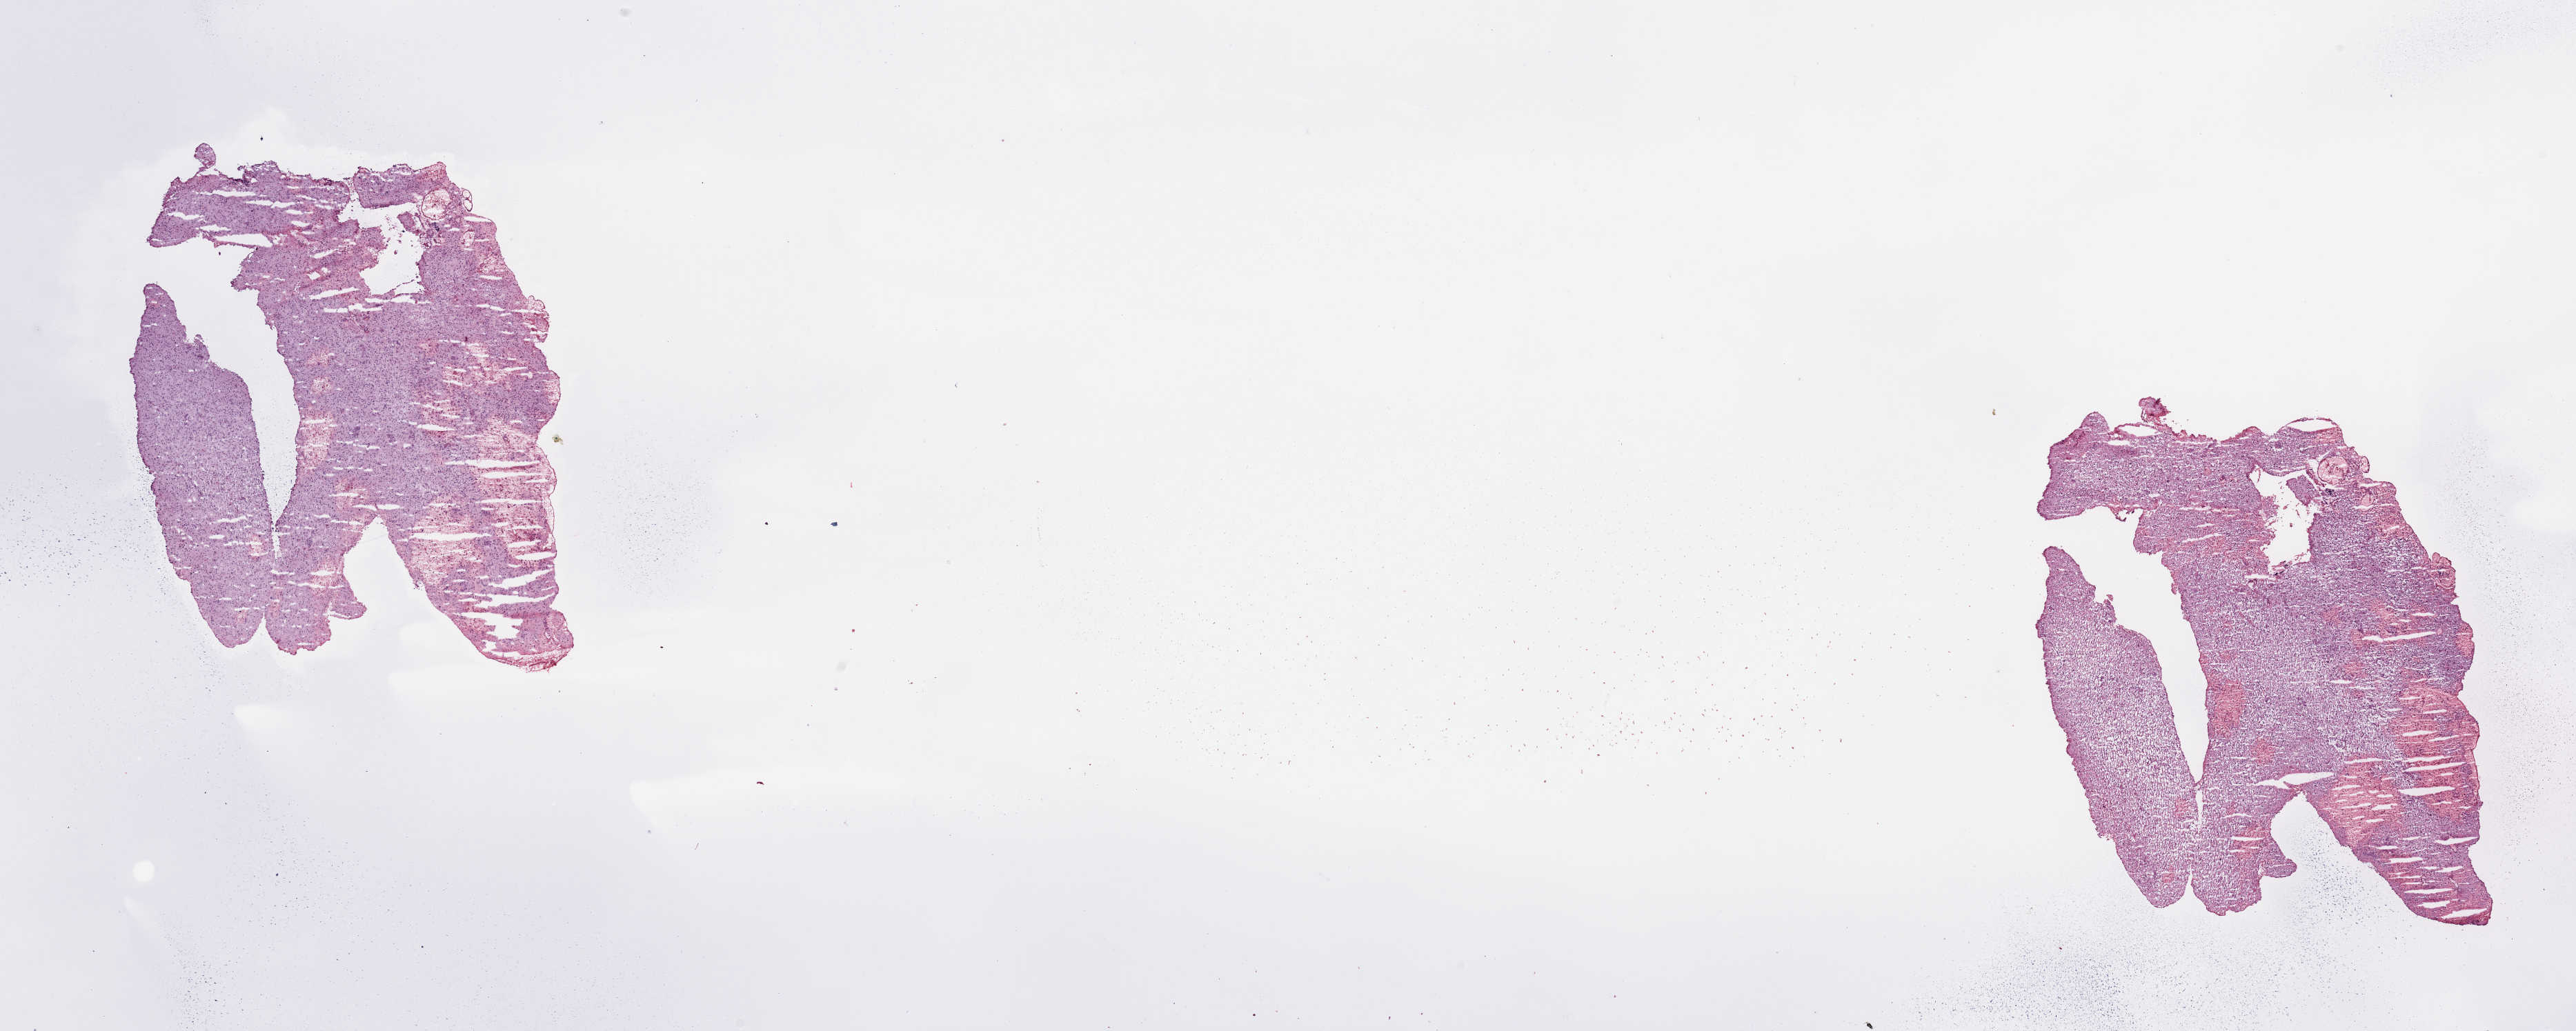
H&E-stained whole-slide image, shown as a low-resolution overview of the whole scanned area (about 29.5 x 11.8 mm, slide scanned at 20x). Tumour tissue sample, brain. Patient: male, age 77 years.
Patient diagnosis (cohort enrolment): glioblastoma multiforme (brain).